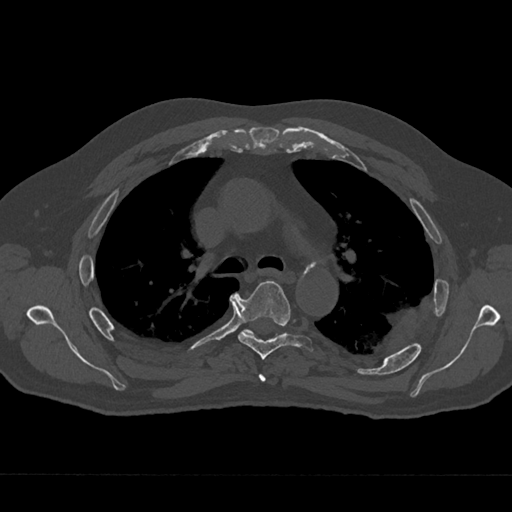
CT including the spine, one axial slice; slice 470 of 797 in the series (ordered by position); reconstruction kernel Br40s/3; 120 kVp; bone window (W 1800 / L 400 HU); 512 × 512 image matrix, field of view 377 × 377 mm. Male patient, age 75 years. Case-level facts recorded for this patient, not image findings: primary cancer: renal; vertebrae with lytic lesions (as recorded): T4.
Structures marked on this image (semi-automatic segmentation, software-assisted and operator-edited):
- T4 vertebra: box from (x=259, y=374) to (x=266, y=382) px
- T5 vertebra: (x=236, y=281)–(x=314, y=359)
- T6 vertebra: (x=244, y=329)–(x=254, y=335)